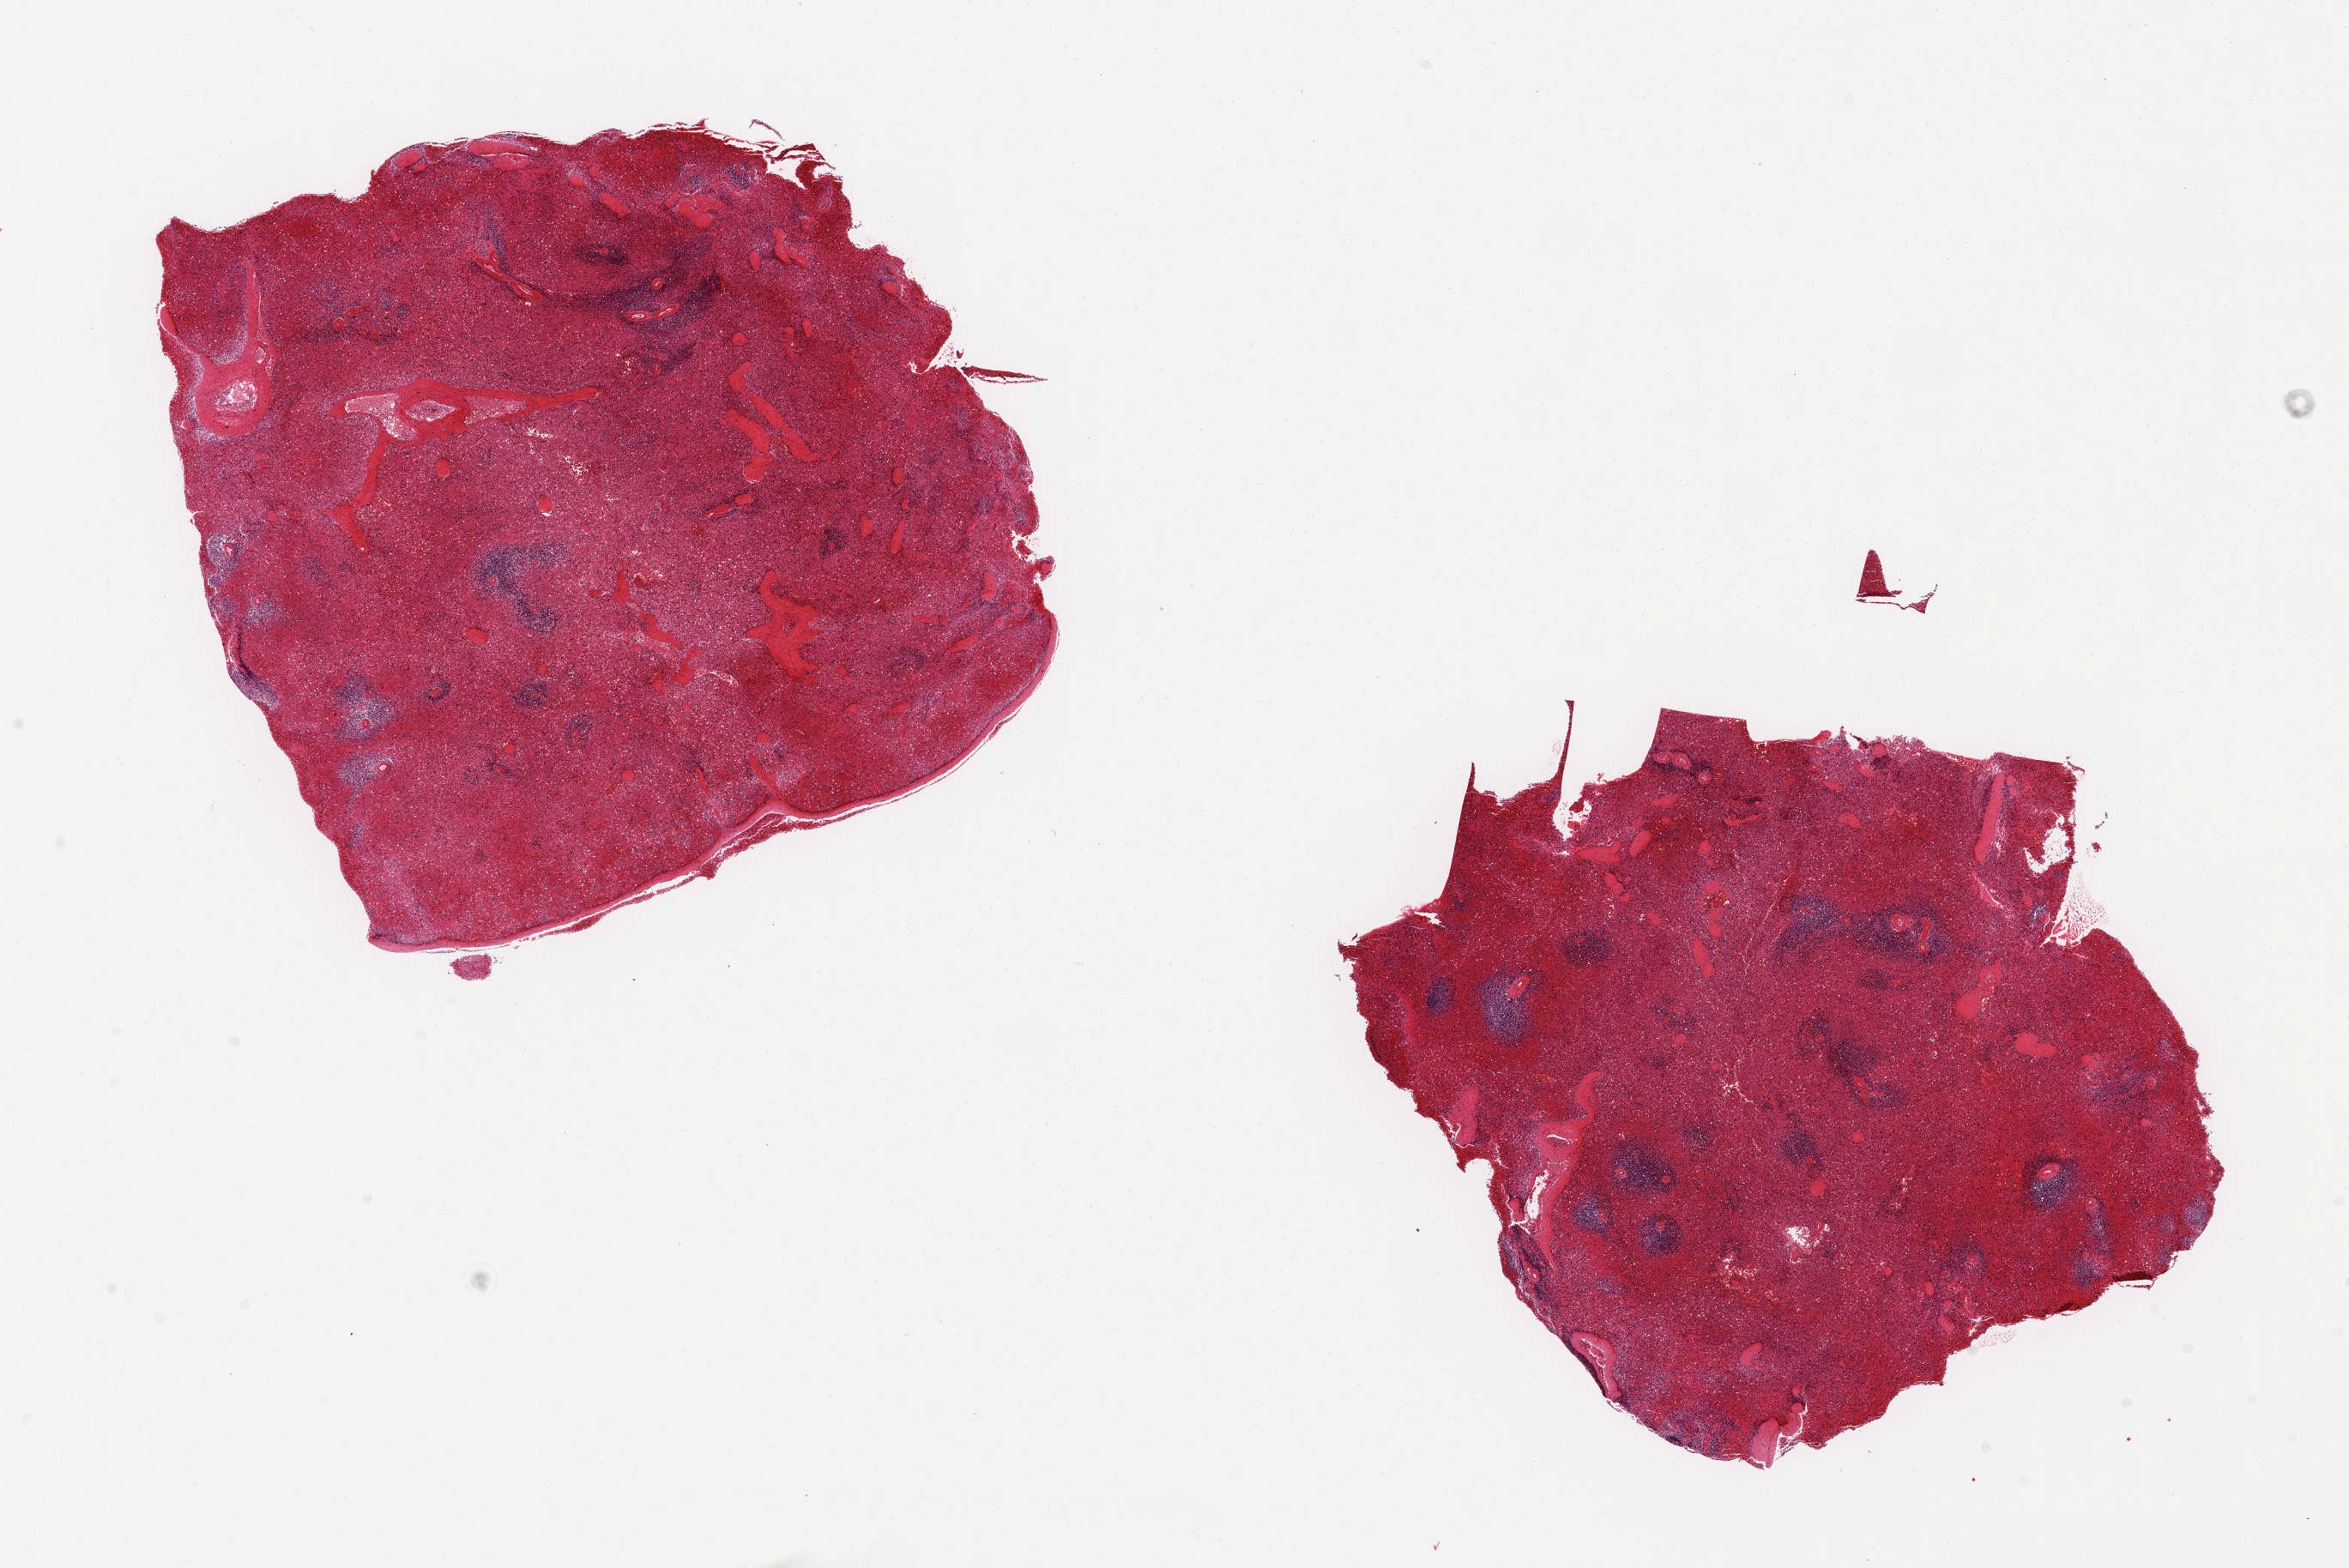
Haematoxylin and eosin whole-slide image, a low-resolution overview of the entire scanned area, about 21.7 x 14.5 mm; PAXgene-fixed paraffin-embedded (PFPE) section; sampled site (target tissue): spleen; donor tissue sample. Donor sex: male.
• pathologist's review note for this sample: 2 pieces,~7mm and 6mm cubed; capsule on one surface; moderately congested